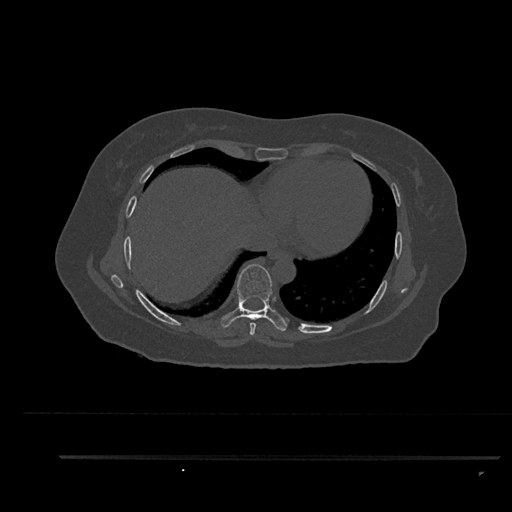
CT including the spine, one axial slice. Slice 468 of 797 in the series (ordered by position). Reconstruction kernel Br40s/3. Bone window (W 1800 / L 400 HU). 512 × 512 image matrix. Patient: female, 44 years. From the clinical record (not read from this slice): primary cancer: renal; vertebrae with lytic lesions (as recorded): L1.
Structures marked on this image (semi-automatic segmentation, software-assisted and operator-edited):
- T7 vertebra: bounding box [x1, y1, x2, y2] px = [249, 322, 256, 336]
- T8 vertebra: [221, 264, 287, 331]